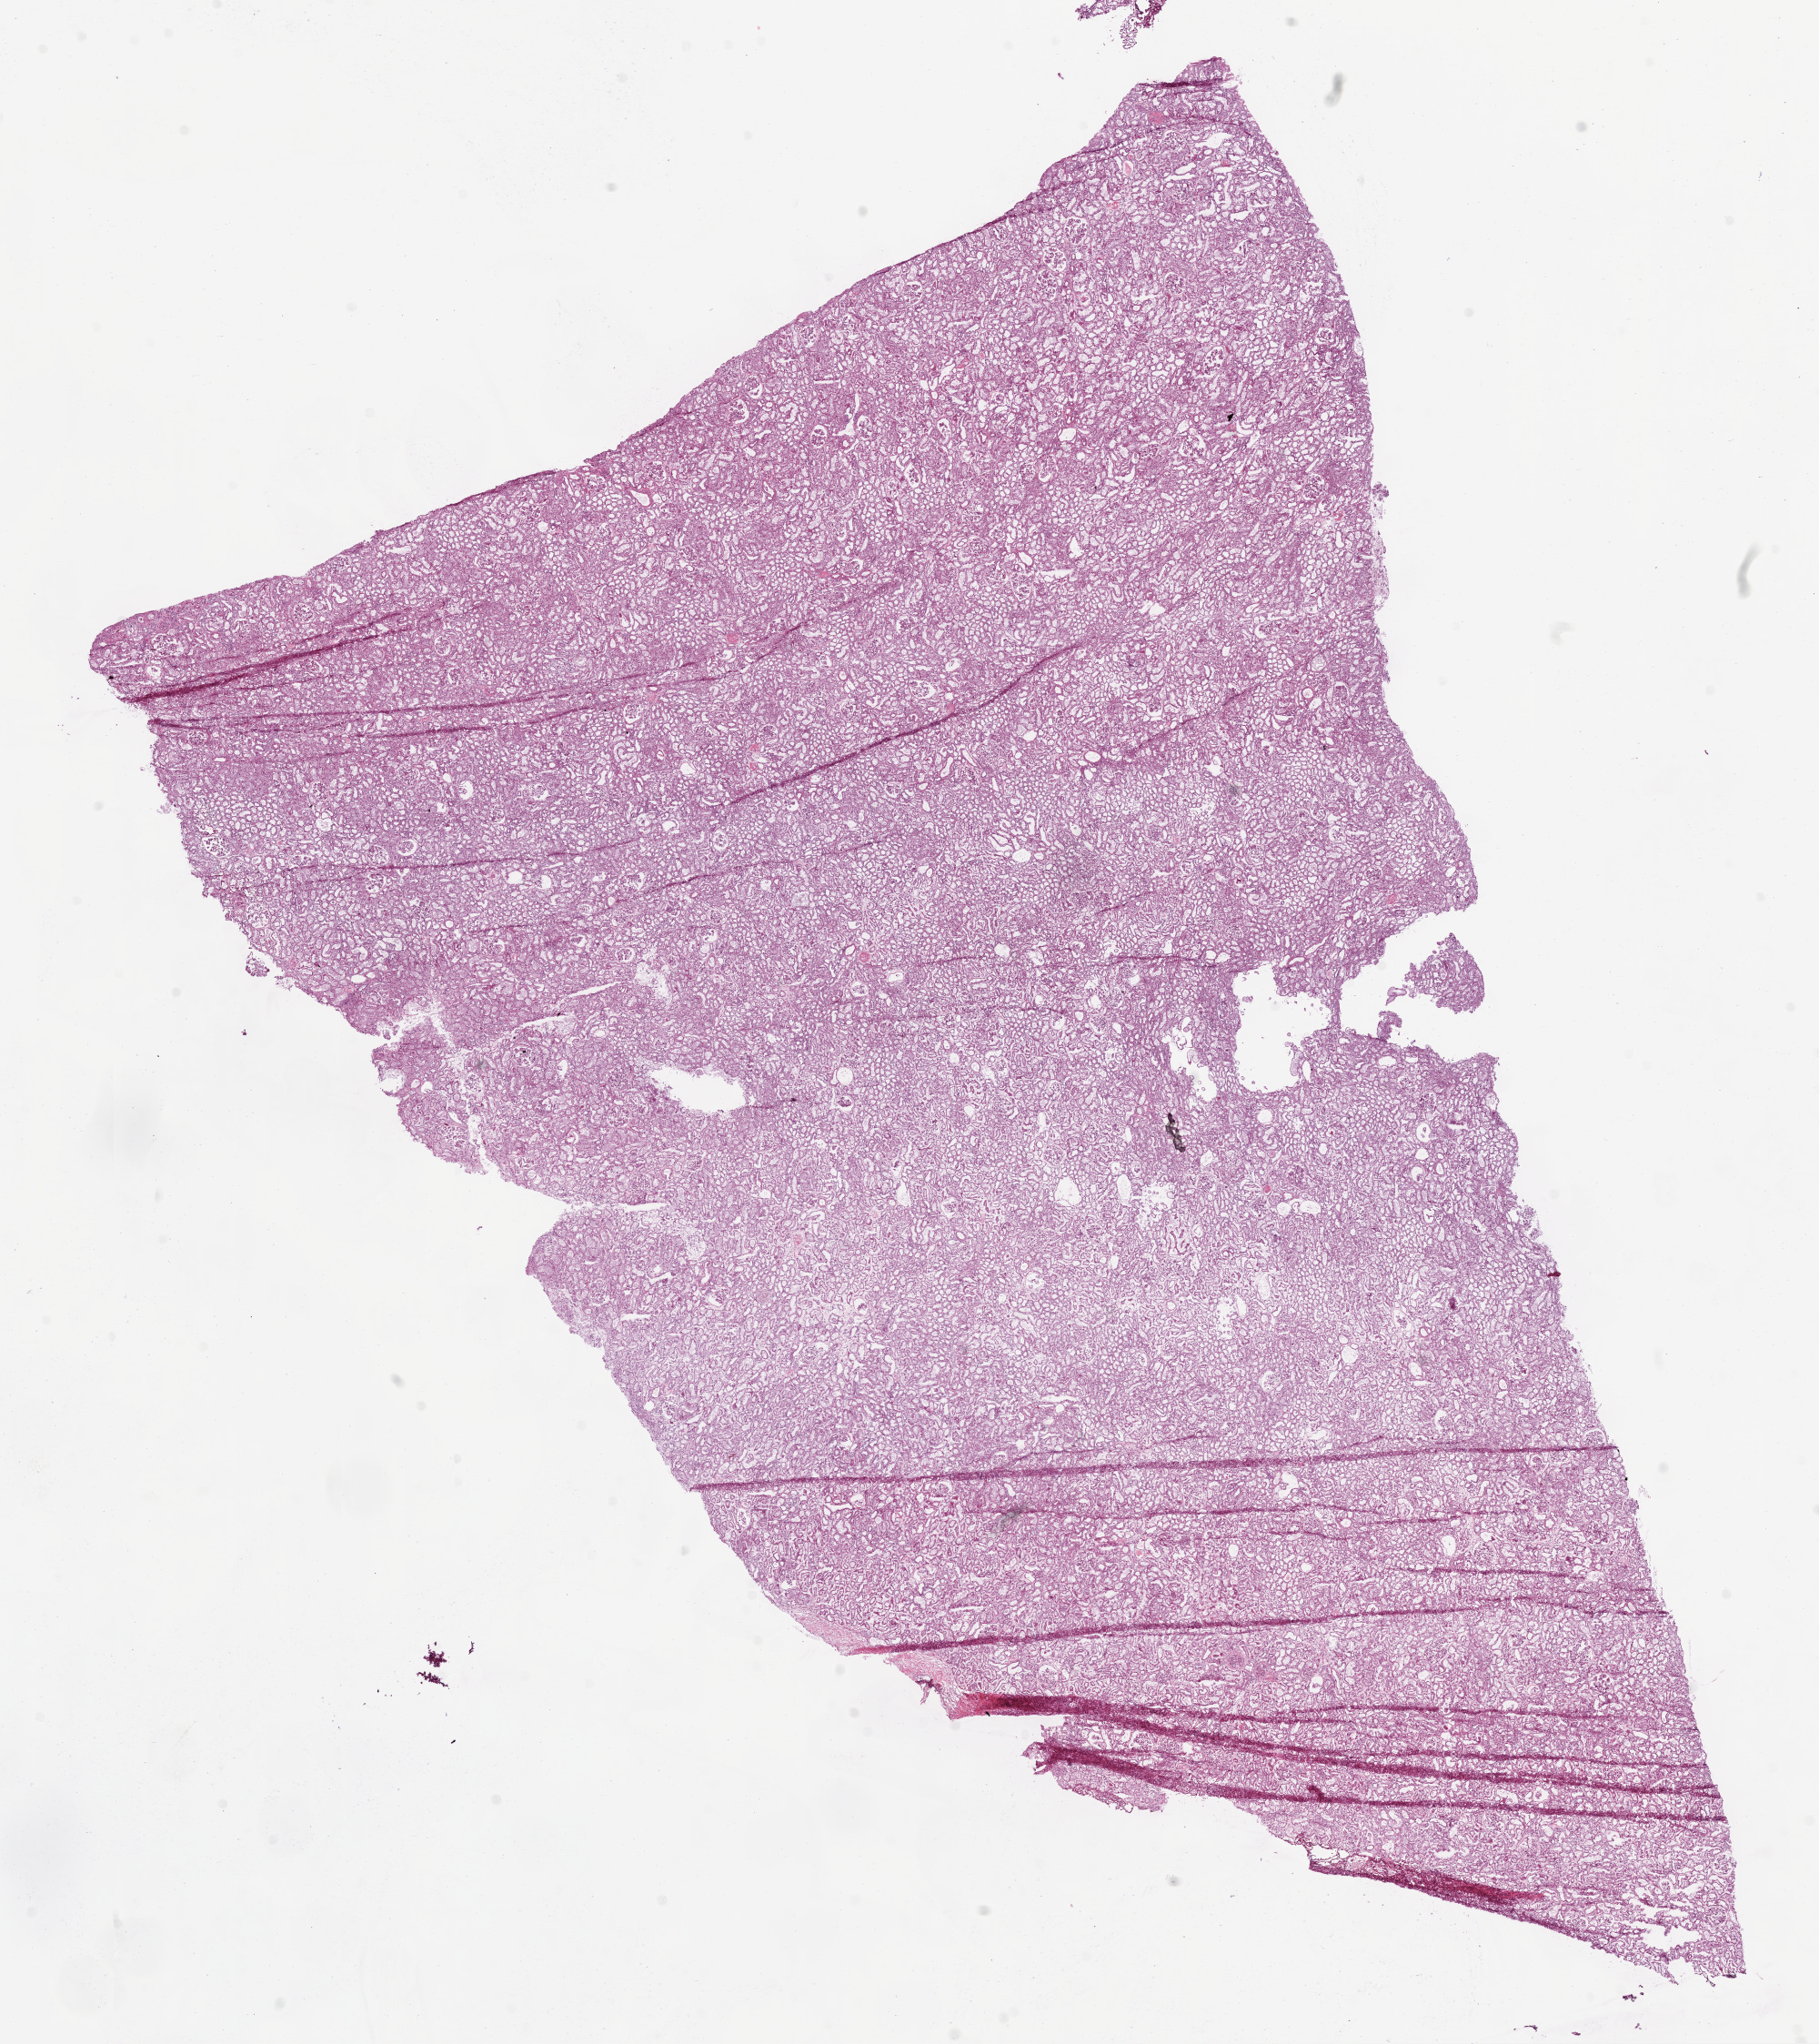
Whole-slide histology image, H&E, shown as a low-resolution overview of the whole scanned area (about 16.0 x 18.0 mm); frozen section from the bottom of the tissue portion; solid tissue normal (non-tumour tissue) sample from the kidney. Female, age 72 years at initial diagnosis.
This section: solid tissue normal sample (biorepository sample class). Patient diagnosis: Clear cell adenocarcinoma, NOS.